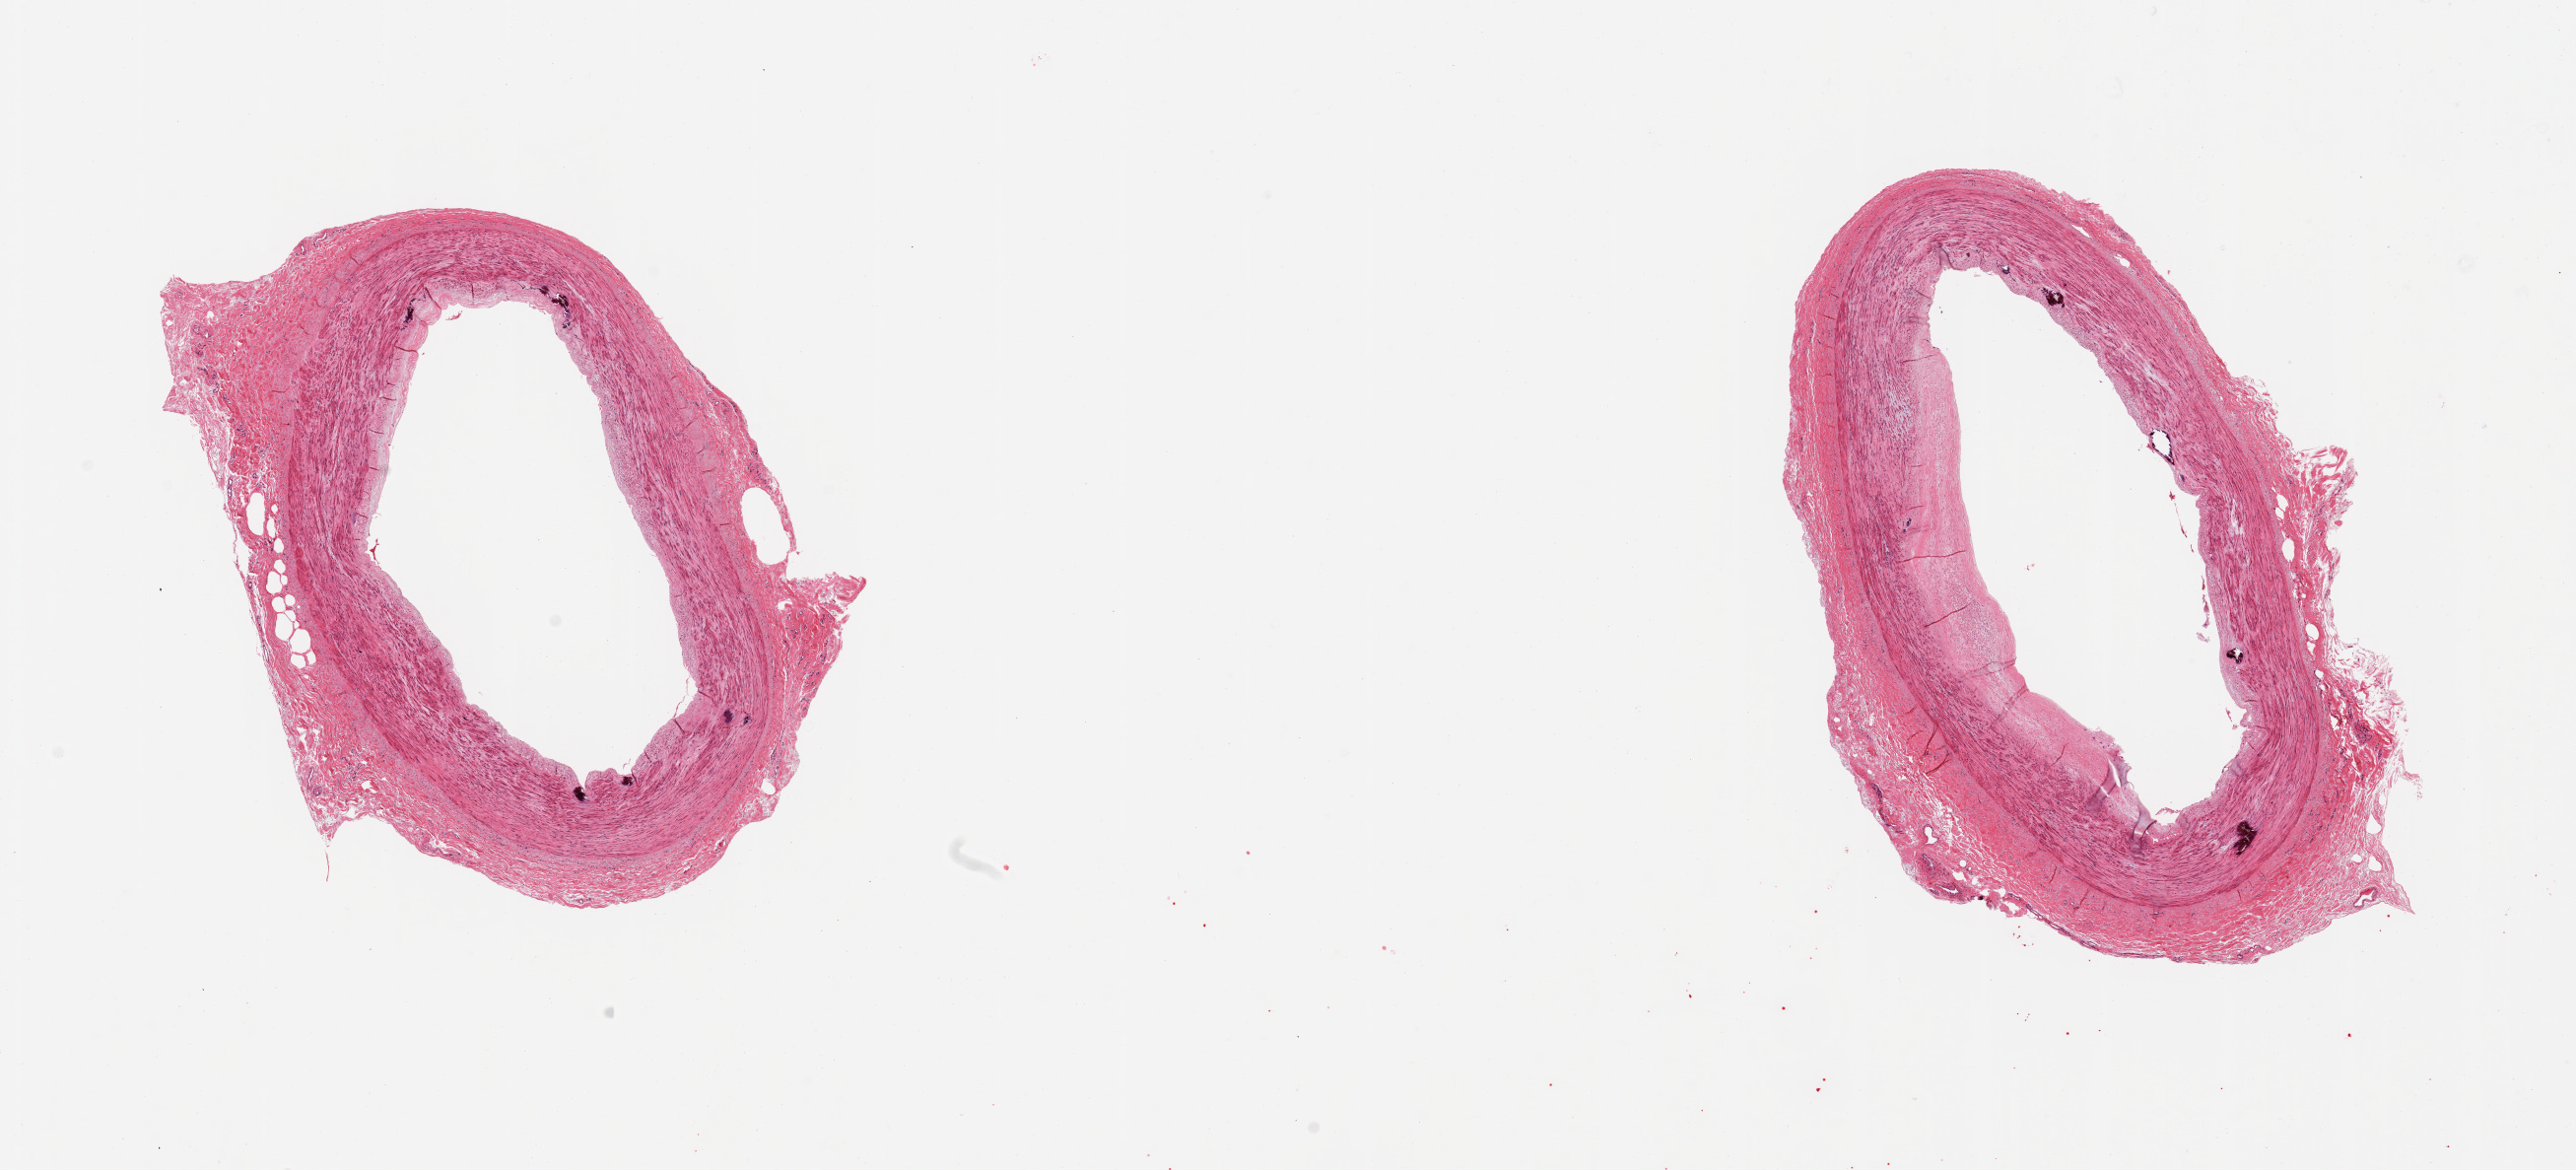
Digitized H&E-stained section, low-resolution overview of the scanned area, about 20.7 x 9.4 mm. PAXgene-fixed paraffin-embedded (PFPE) section. Section of tibial artery (target tissue). Donor tissue sample. Donor: male.
* reviewer comment on this tissue sample: 2 pieces; well trimmed; flat intimal plaque; several small focal calcium deposits in media and intima